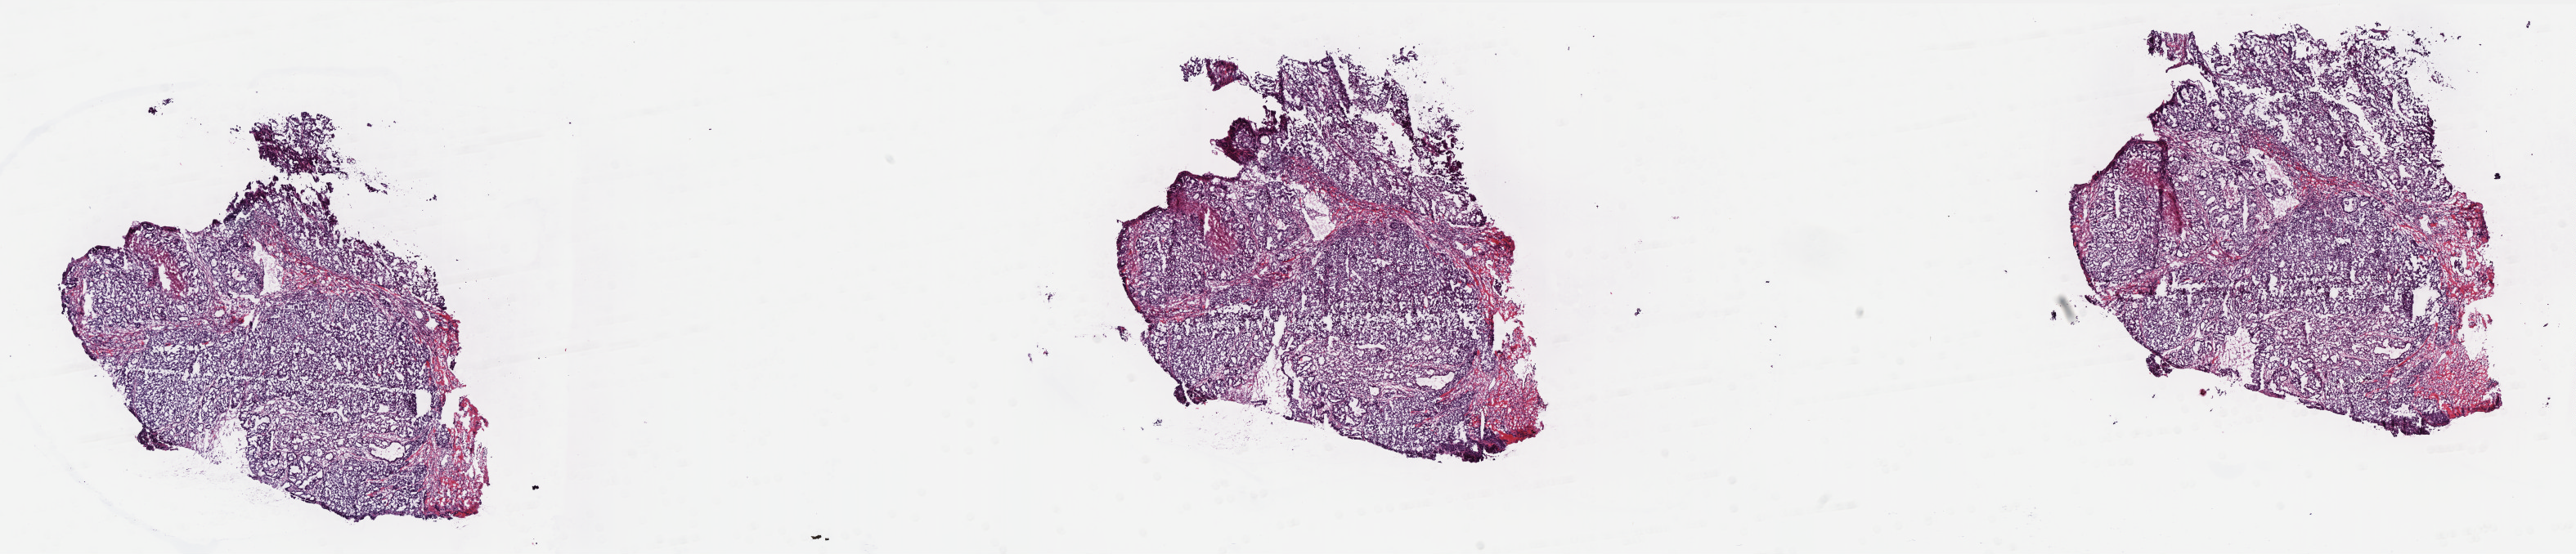
Whole-slide histology image, H&E-stained, a low-resolution overview of the entire scanned area, about 25.3 x 5.4 mm, frozen section from the bottom of the tissue portion, primary tumour sample from the breast. Female, age 41 years at initial diagnosis. Slide review estimates, as recorded: tumour cells 80%, tumour nuclei 80%, normal cells 0%, stromal cells 15%, necrosis 5%. Infiltration values recorded for this section: lymphocyte infiltration 10%, monocyte infiltration 15%, neutrophil infiltration 5%.
Lymph nodes positive (case pathology): 0 of 5 examined. Pathologic diagnosis: Infiltrating duct carcinoma, NOS. AJCC pathologic stage: IIIB (7th edition). TNM: T4 N0 M0.